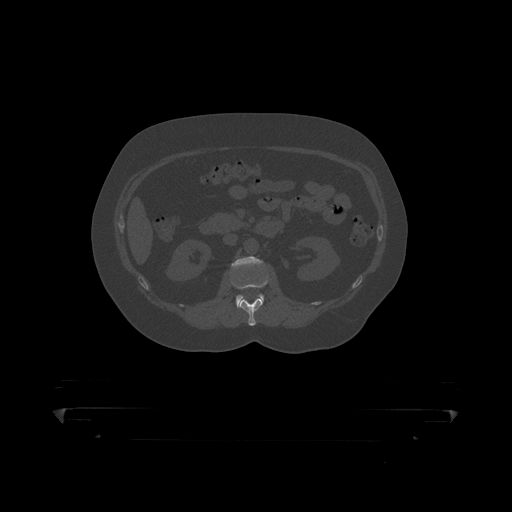
CT including the spine, one axial slice; slice 133 of 390 in the series (ordered by position); bone window (W 1800 / L 400 HU); 1.25 mm slice thickness; 512 × 512 image matrix, field of view 650 × 650 mm. Male patient, age 60 years. Case-level facts recorded for this patient, not image findings: primary cancer: prostate.
Outlined on this slice (semi-automatically segmented with operator editing):
- L1 vertebra: bounding box <232,277,269,319> (left, top, right, bottom; pixels)
- L2 vertebra: <232,256,264,308>